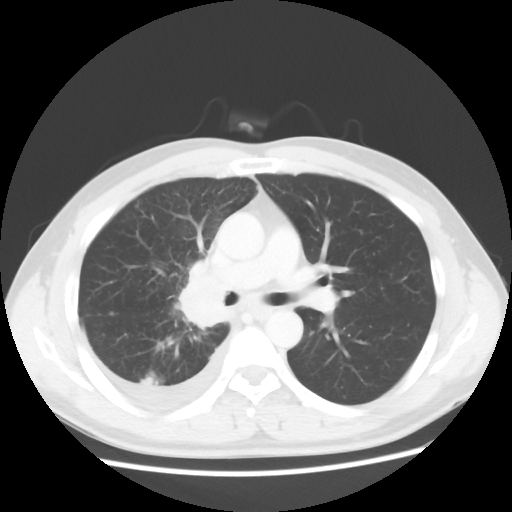
Chest CT, one axial slice. Slice 33 of 56 in the series (ordered by position). Reconstruction kernel STANDARD. Lung window (W 1500 / L -600 HU). 5 mm slice thickness. 512 × 512 image matrix, field of view 360 × 360 mm. Male patient, age 46 years. From the clinical record (not read from this slice): clinical TNM (as recorded): T2 N3 M1.
Structures marked on this image (rectangle marked by the reading radiologist):
- lung tumour (recorded histology: adenocarcinoma): bounding box [x1, y1, x2, y2] px = [175, 268, 227, 330]